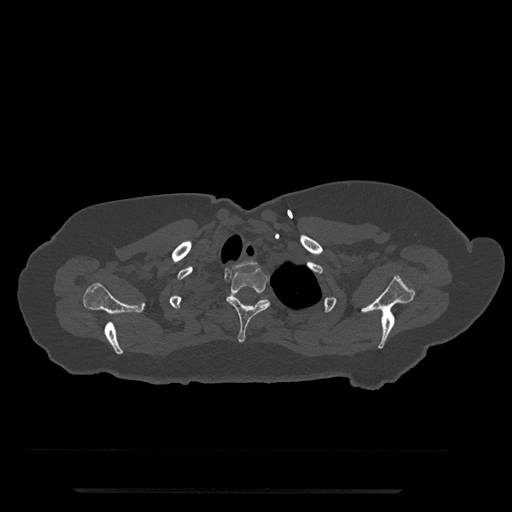
CT including the spine, one axial slice. Position 669 of 797 along the scan axis. Reconstruction kernel Br40s/3. 120 kVp. Bone window (W 1800 / L 400 HU). 512 × 512 image matrix. Female patient, age 51 years. From the clinical record (not read from this slice): primary cancer: neuro; vertebrae with lytic lesions (as recorded): T8.
Structures marked on this image (semi-automatic segmentation, software-assisted and operator-edited):
- T1 vertebra: bounding box [x1, y1, x2, y2] px = [233, 261, 254, 268]
- T2 vertebra: [226, 267, 271, 343]
- T3 vertebra: [233, 293, 269, 305]